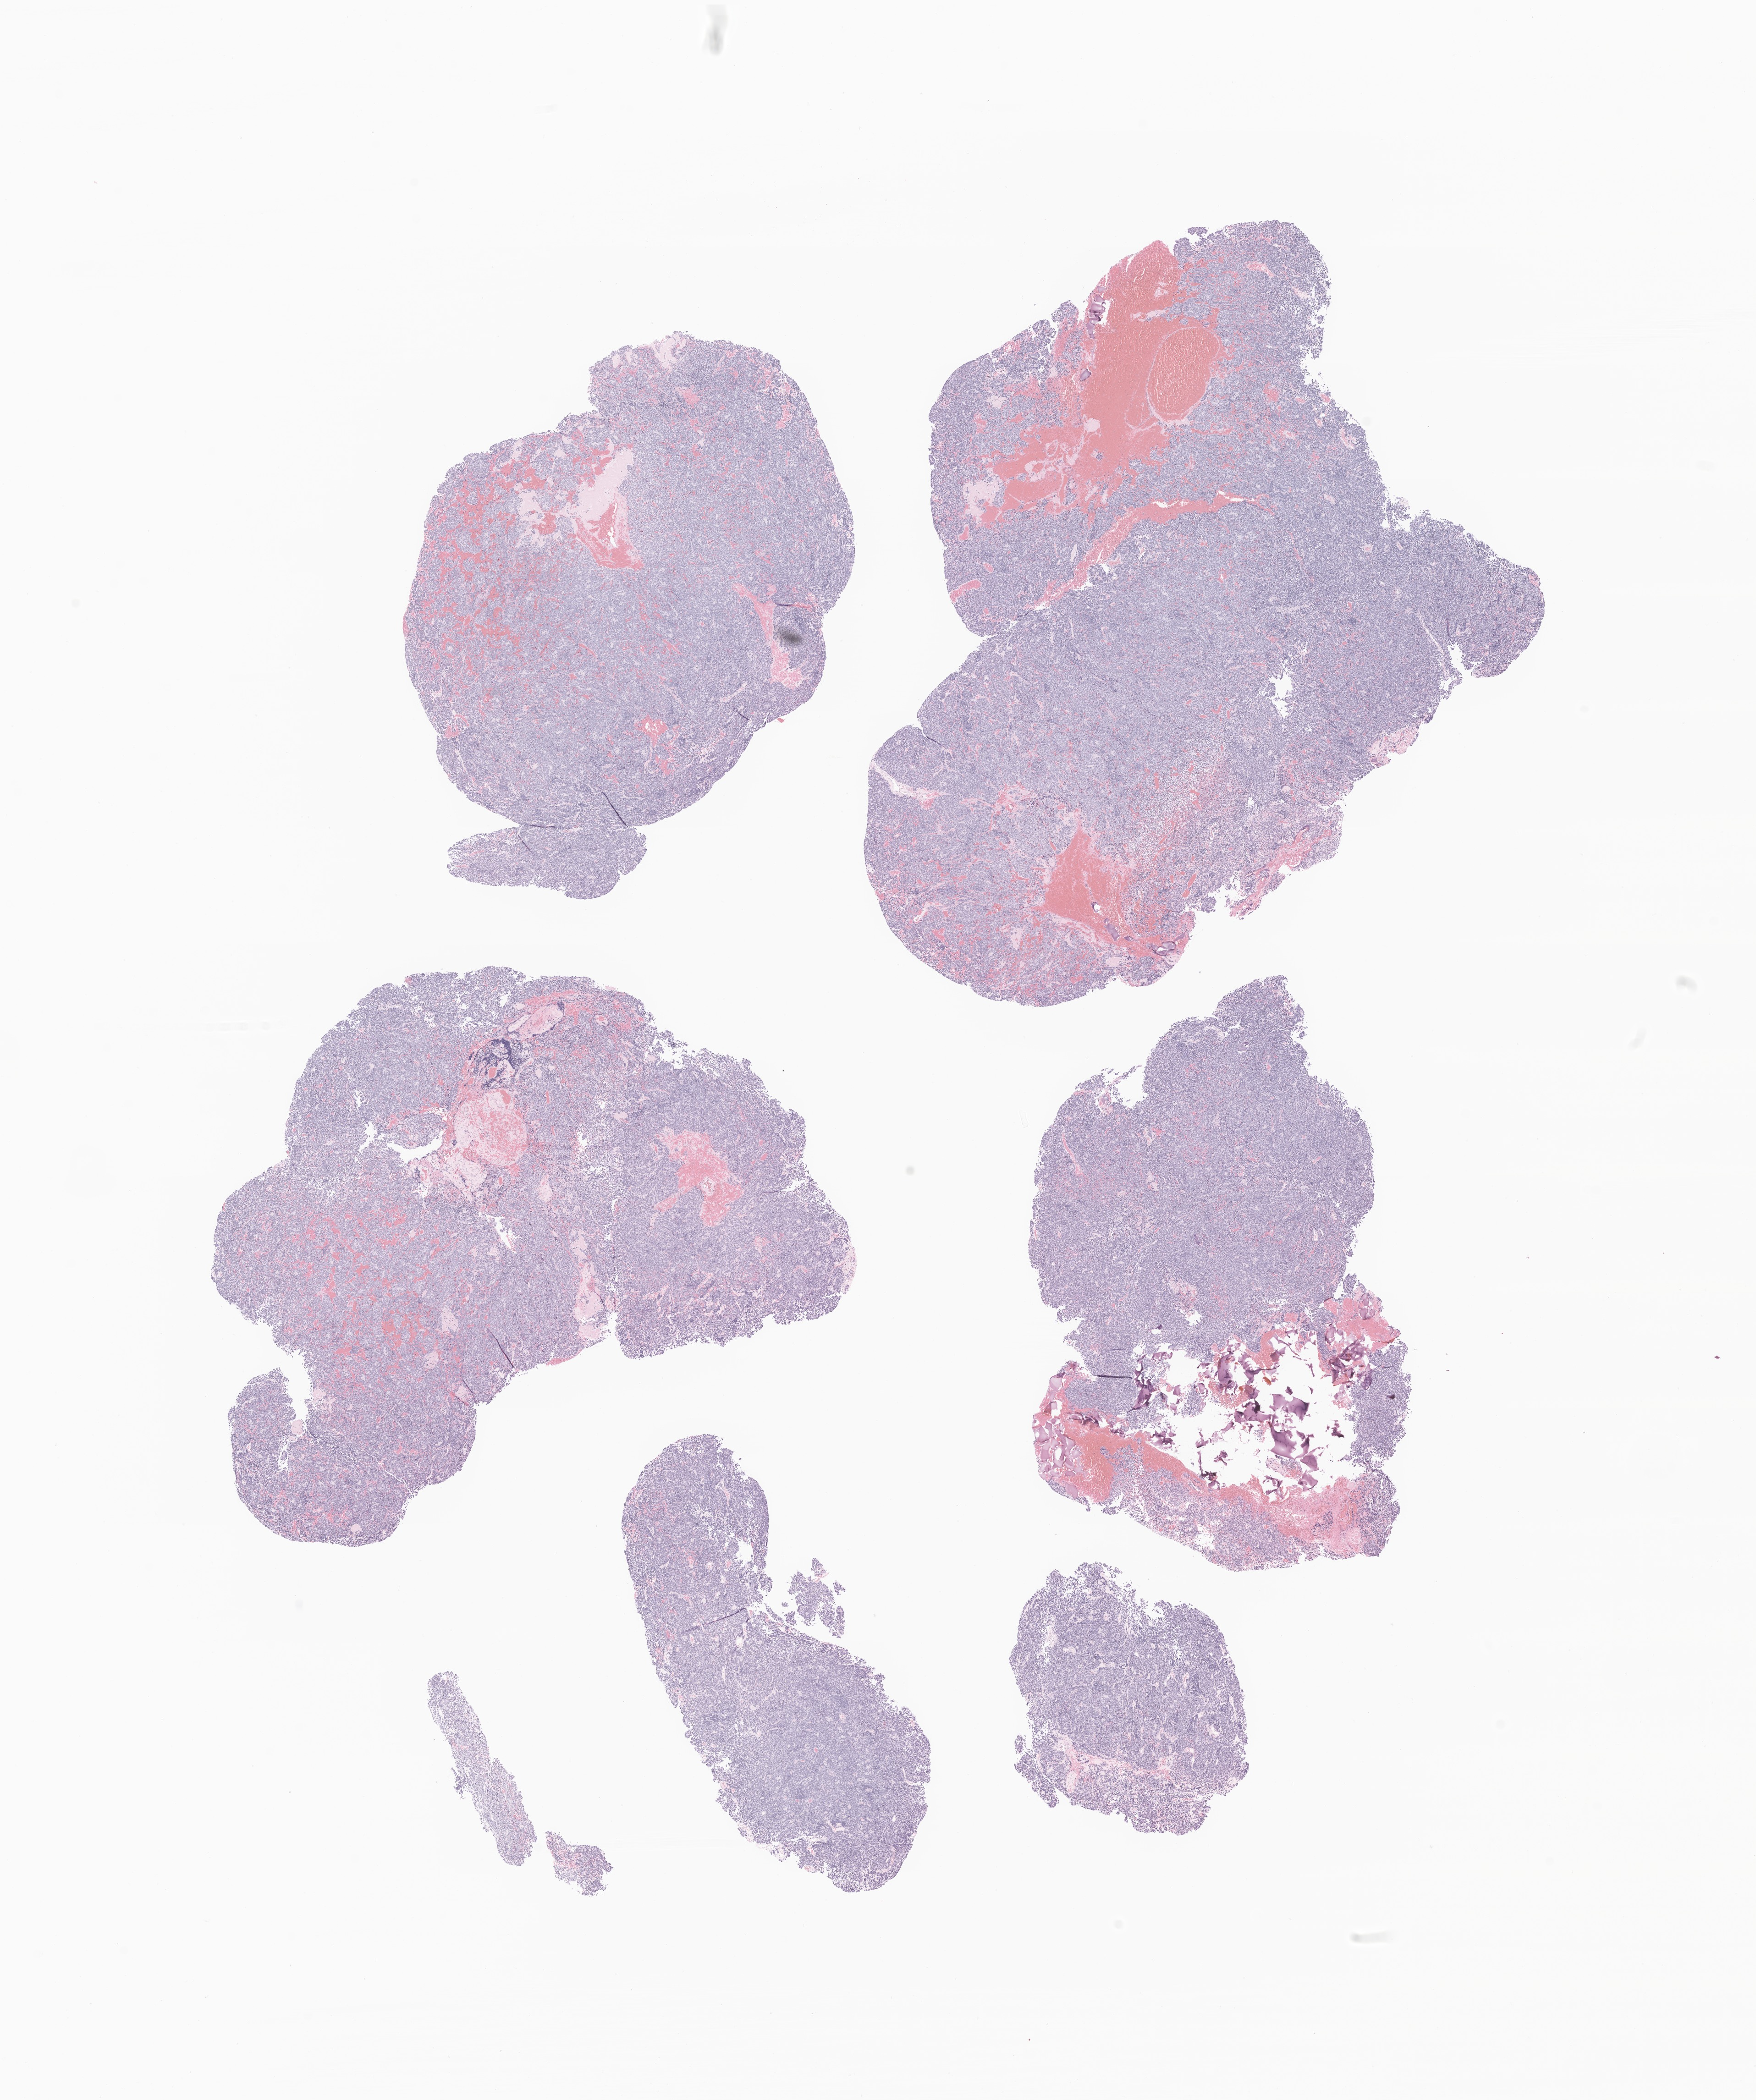
Whole-slide image, hematoxylin and eosin (H&E) stain of tumor tissue from the cerebral ventricle — whole scanned area (about 16.2 x 19.3 mm) shown as a low-resolution overview; formalin-fixed paraffin-embedded section. Patient female; age 80 months (6 years 8 months).
Recorded diagnosis: Medulloblastoma, NOS.